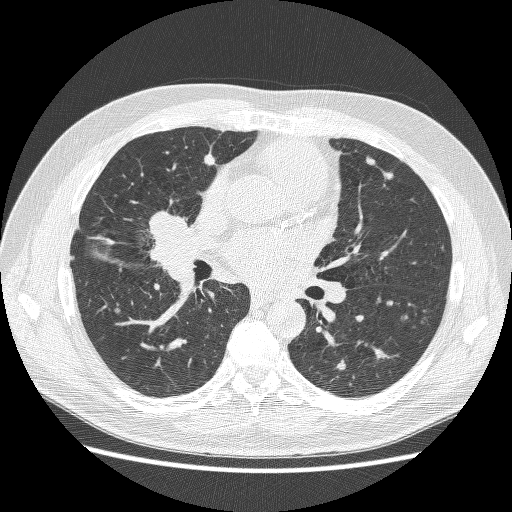
Axial slice from a low-dose chest CT screening exam; baseline annual screen; lung window (W 1500 / L -600 HU); lung (sharp) reconstruction kernel (BONE); 512 × 512 image matrix. Male participant, aged 59 years at enrolment. Former smoker at enrolment.
Expert reader's lesion annotation, bounding box (x1, y1, x2, y2) in pixels: (126, 202, 197, 269). No non-calcified nodule or mass ≥4 mm was recorded by the screening reader at this exam. Official screen result: positive, change unspecified: nodule(s) >= 4 mm or enlarging nodule(s), mass(es), or other non-specific abnormalities suspicious for lung cancer. Participant outcome: lung cancer diagnosed 24 days after this screen — adenocarcinoma, NOS, right middle lobe, poorly differentiated (G3), stage IV (AJCC 6th edition), 54 mm at pathology.